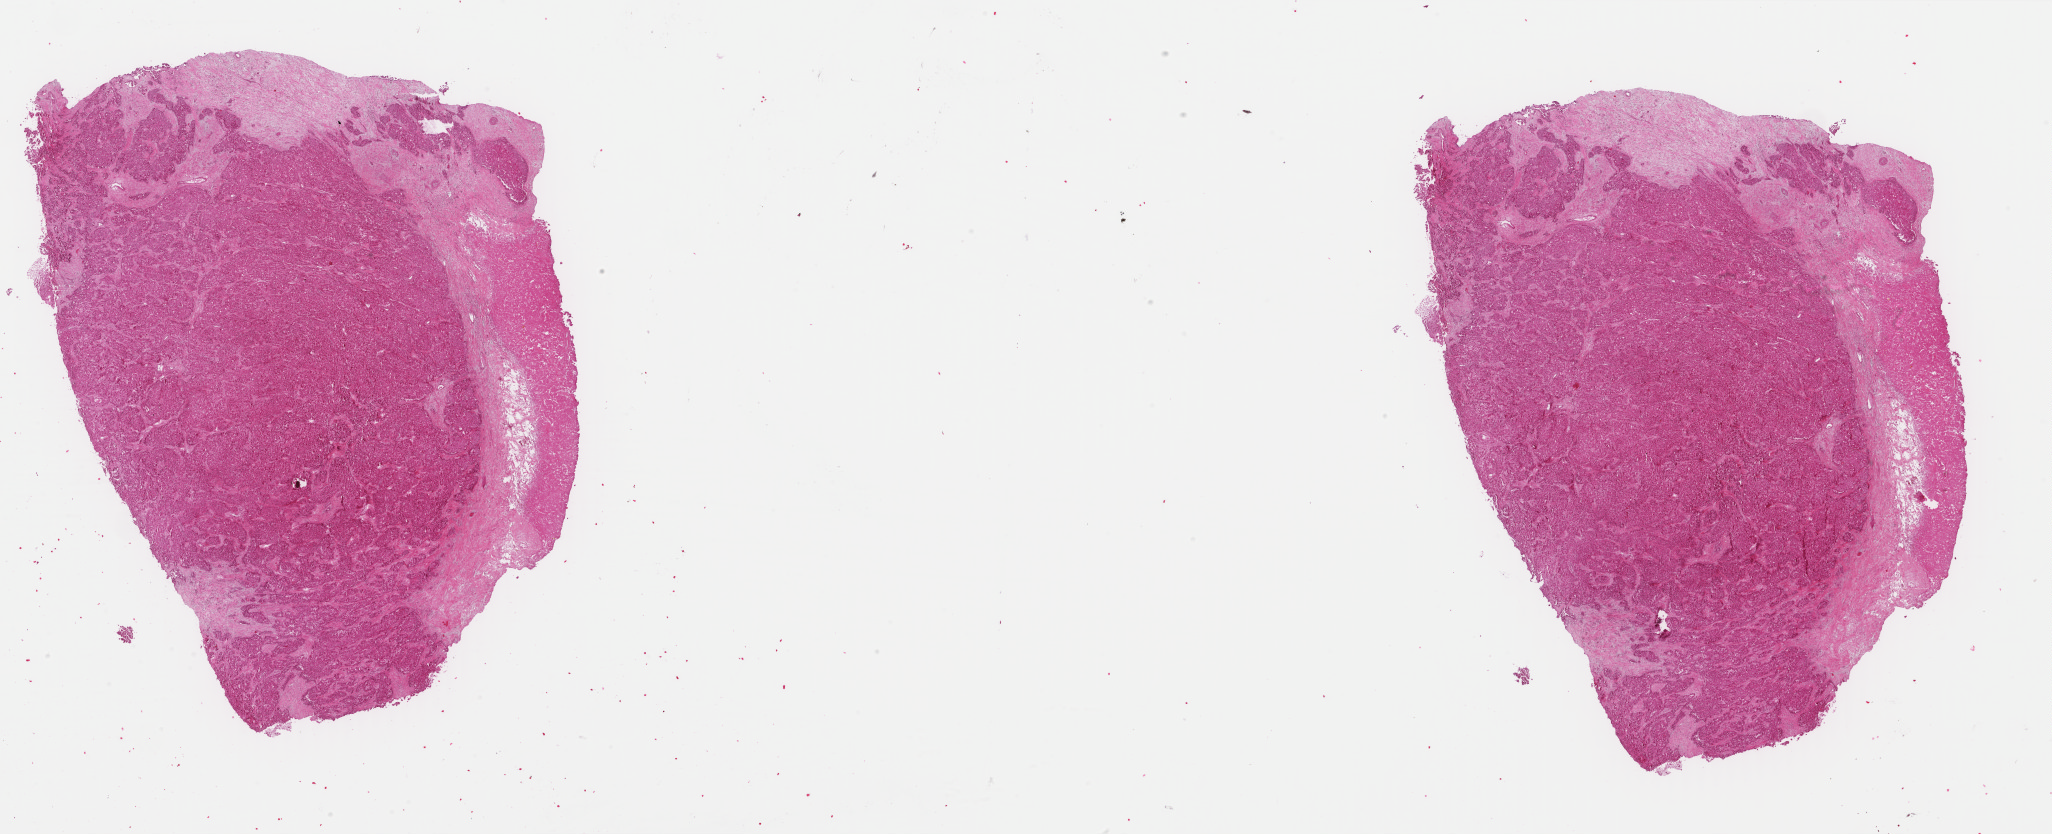
H&E whole-slide image, whole scanned area (about 32.6 x 13.2 mm, acquisition: 40x scan) shown as a low-resolution overview. FFPE section. Sample: primary tumour, liver. Female patient; age at initial diagnosis 66 years. Histologic grade: G2 (moderately differentiated).
* pathologic diagnosis: Hepatocellular carcinoma, NOS